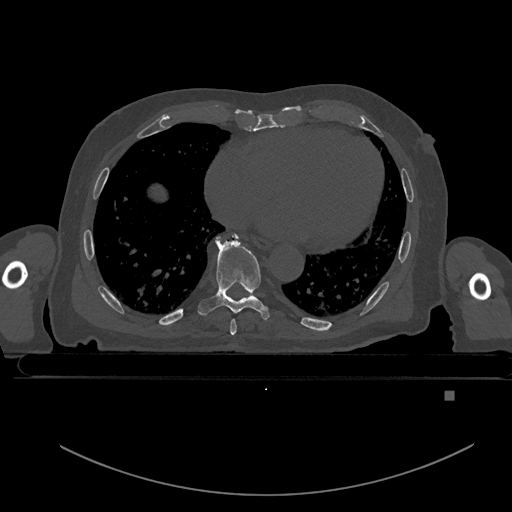
CT including the spine, one axial slice. Slice 203 of 969 in the series (ordered by position). Bone window (W 1800 / L 400 HU). 0.5 mm slice thickness. 512 × 512 image matrix. Male patient, age 82 years. From the clinical record (not read from this slice): primary cancer: prostate; vertebrae with lytic lesions (as recorded): T11, T9, T8, T2.
Annotated regions visible in this slice (semi-automatically segmented with operator editing):
- T7 vertebra: bounding box (x1, y1, x2, y2) in pixels: (230, 319, 236, 335)
- T8 vertebra: (198, 234, 272, 320)